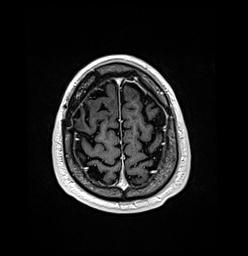
Brain MRI from a brain-tumour surgery series, one axial slice. Slice 28 of 176 in the series (ordered by position). T1-weighted post-contrast. 248 × 256 image matrix, field of view 242 × 250 mm. Case-level facts recorded for this patient, not image findings: histopathology: Oligodendroglioma; WHO grade: 3; IDH mutation: yes.
Structures marked on this image (manually delineated by an expert):
- previous resection cavity: bounding box (x1, y1, x2, y2) in pixels: (73, 107, 82, 120)